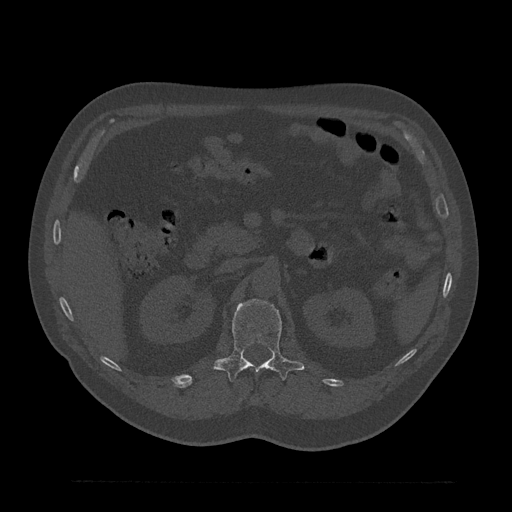
CT including the spine, one axial slice. Slice 172 of 797 in the series (ordered by position). Reconstruction kernel Br40s/3. Bone window (W 1800 / L 400 HU). 512 × 512 image matrix. Patient: male, 61 years. Case-level facts recorded for this patient, not image findings: primary cancer: prostate.
Outlined on this slice (semi-automatic segmentation, software-assisted and operator-edited):
- L1 vertebra: bounding box (x1, y1, x2, y2) in pixels: (214, 299, 304, 383)